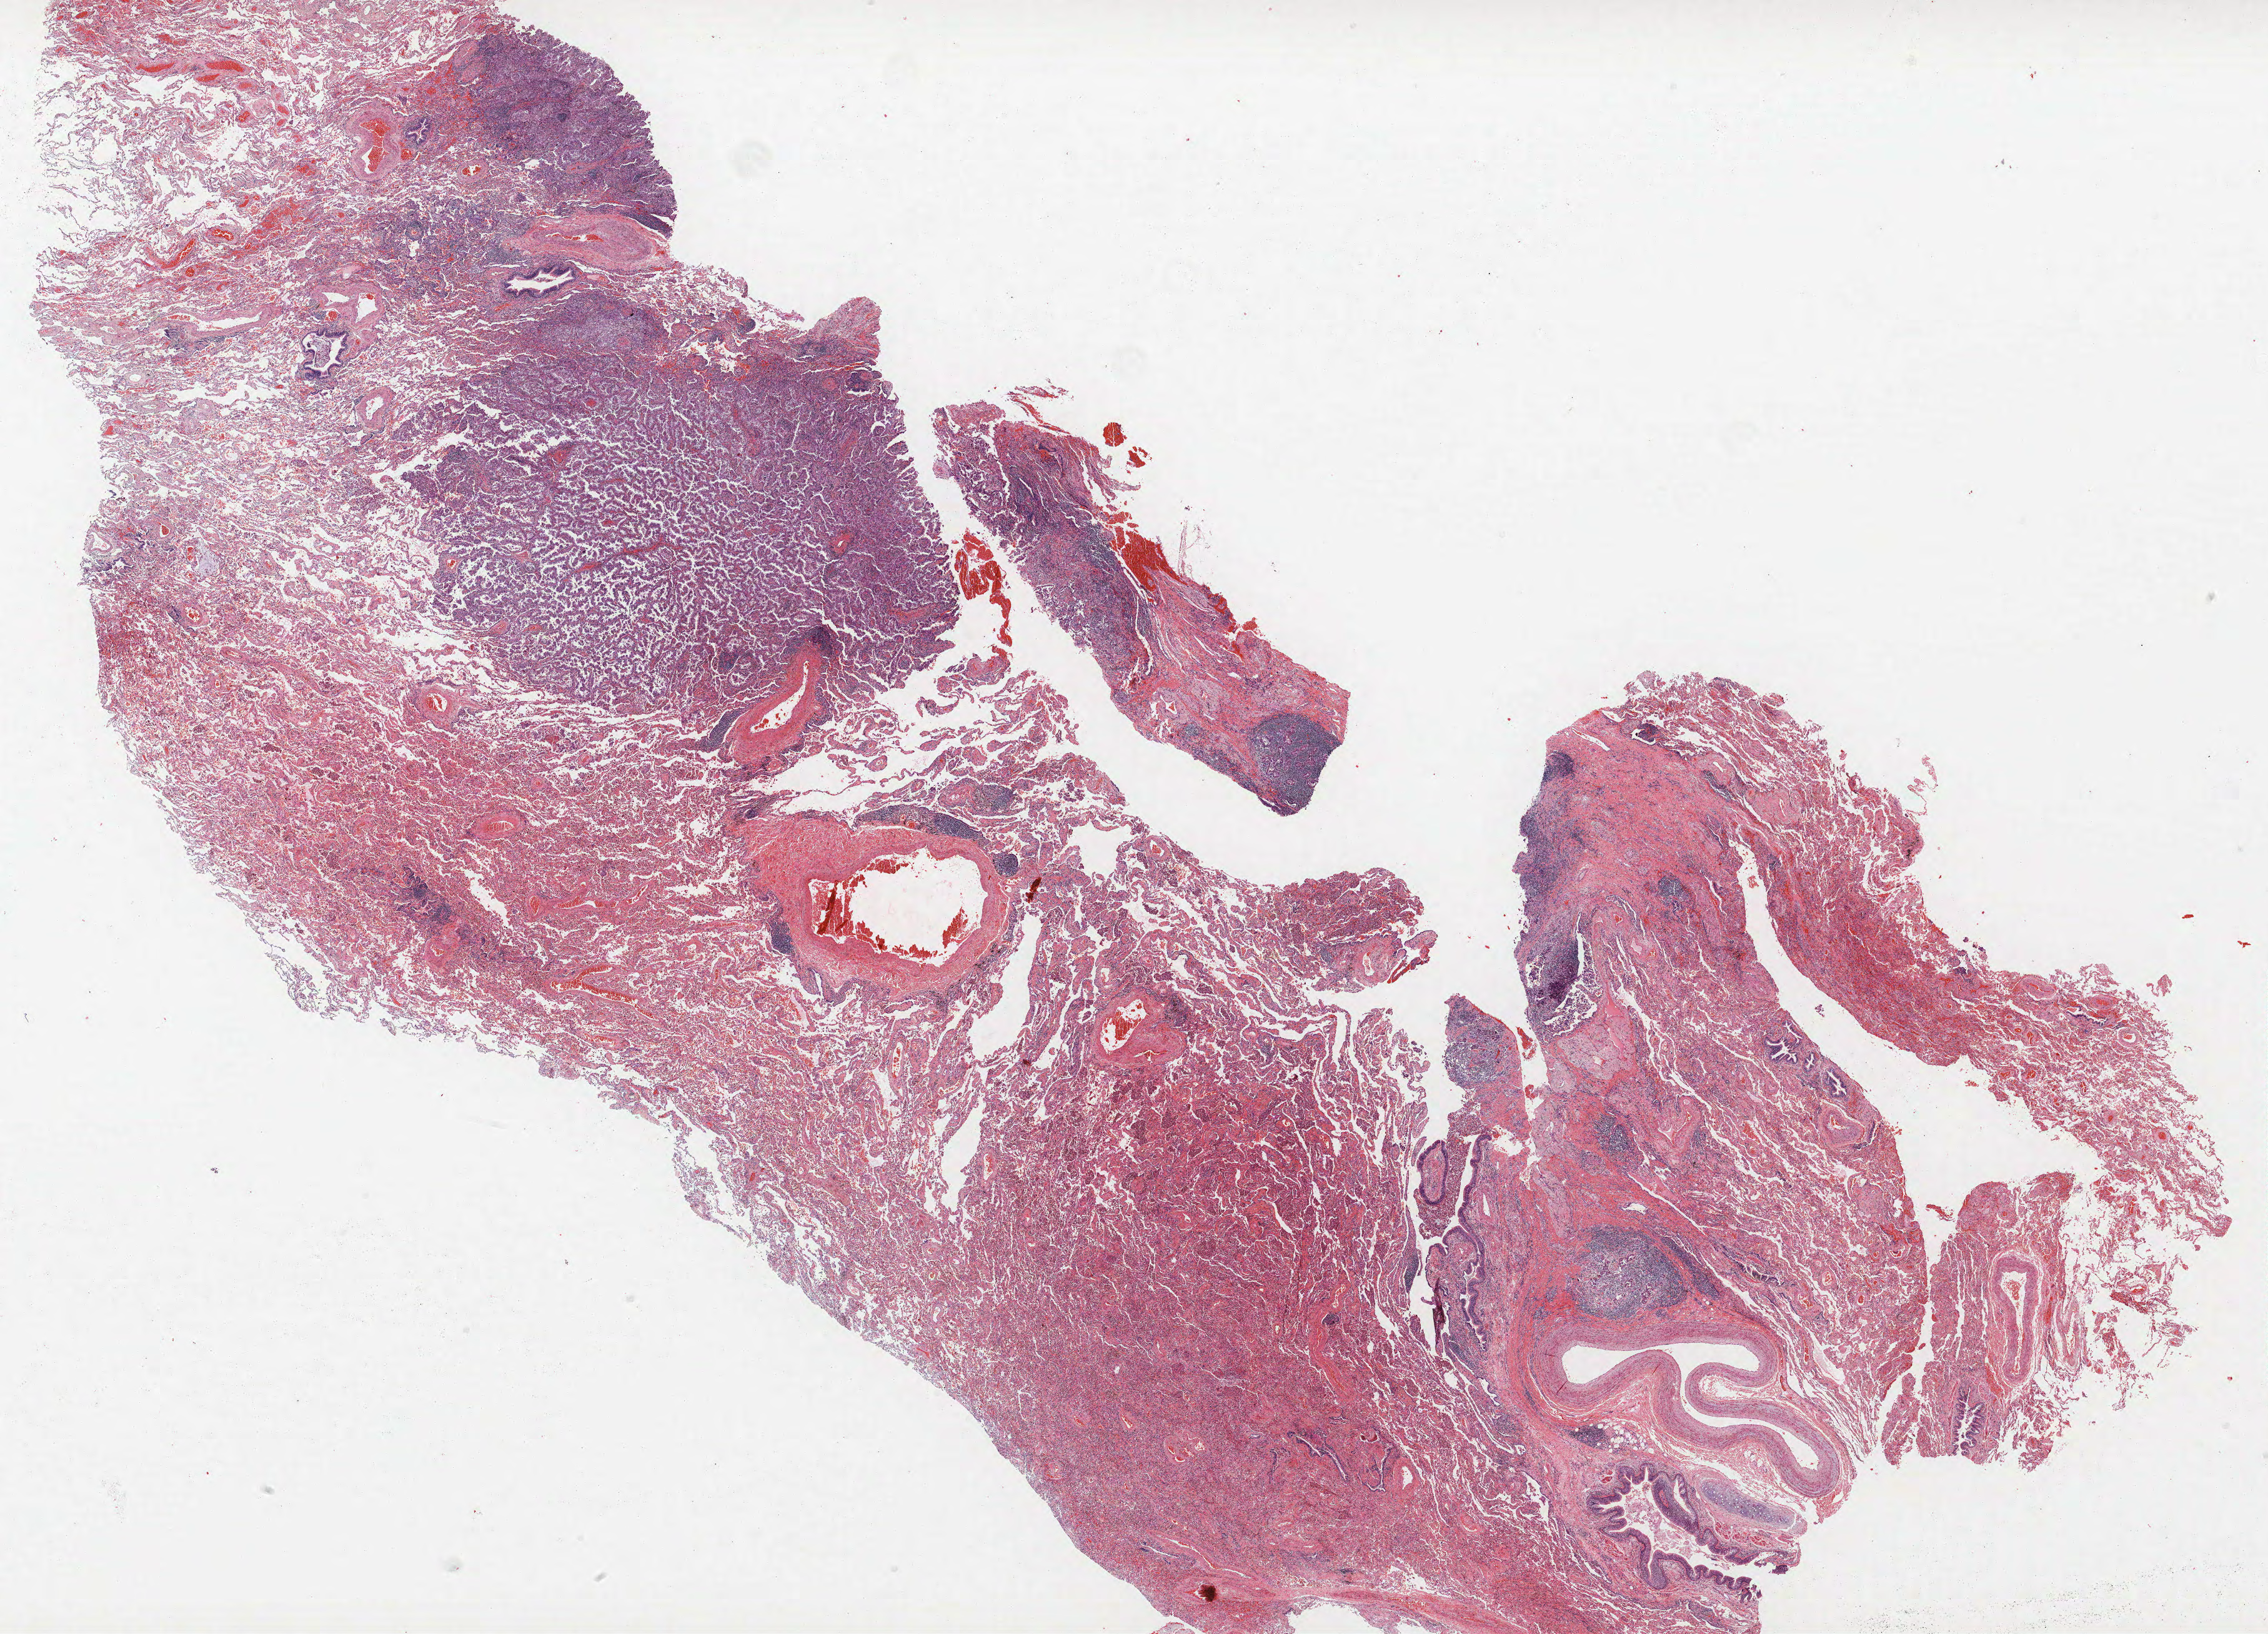
Hematoxylin and eosin (H&E) stained whole-slide image — shown as a low-resolution overview of the whole scanned area (about 29.0 x 20.9 mm), FFPE section, lung tissue. Male patient, aged 71 at enrolment. Current smoker at enrolment. Grade: moderately differentiated (G2).
Stage (AJCC 6th edition): IA. Tumour size (pathology): 24 mm. Primary tumour location (clinical record): right lower lobe. Participant's lung-cancer diagnosis: Adenocarcinoma, NOS.